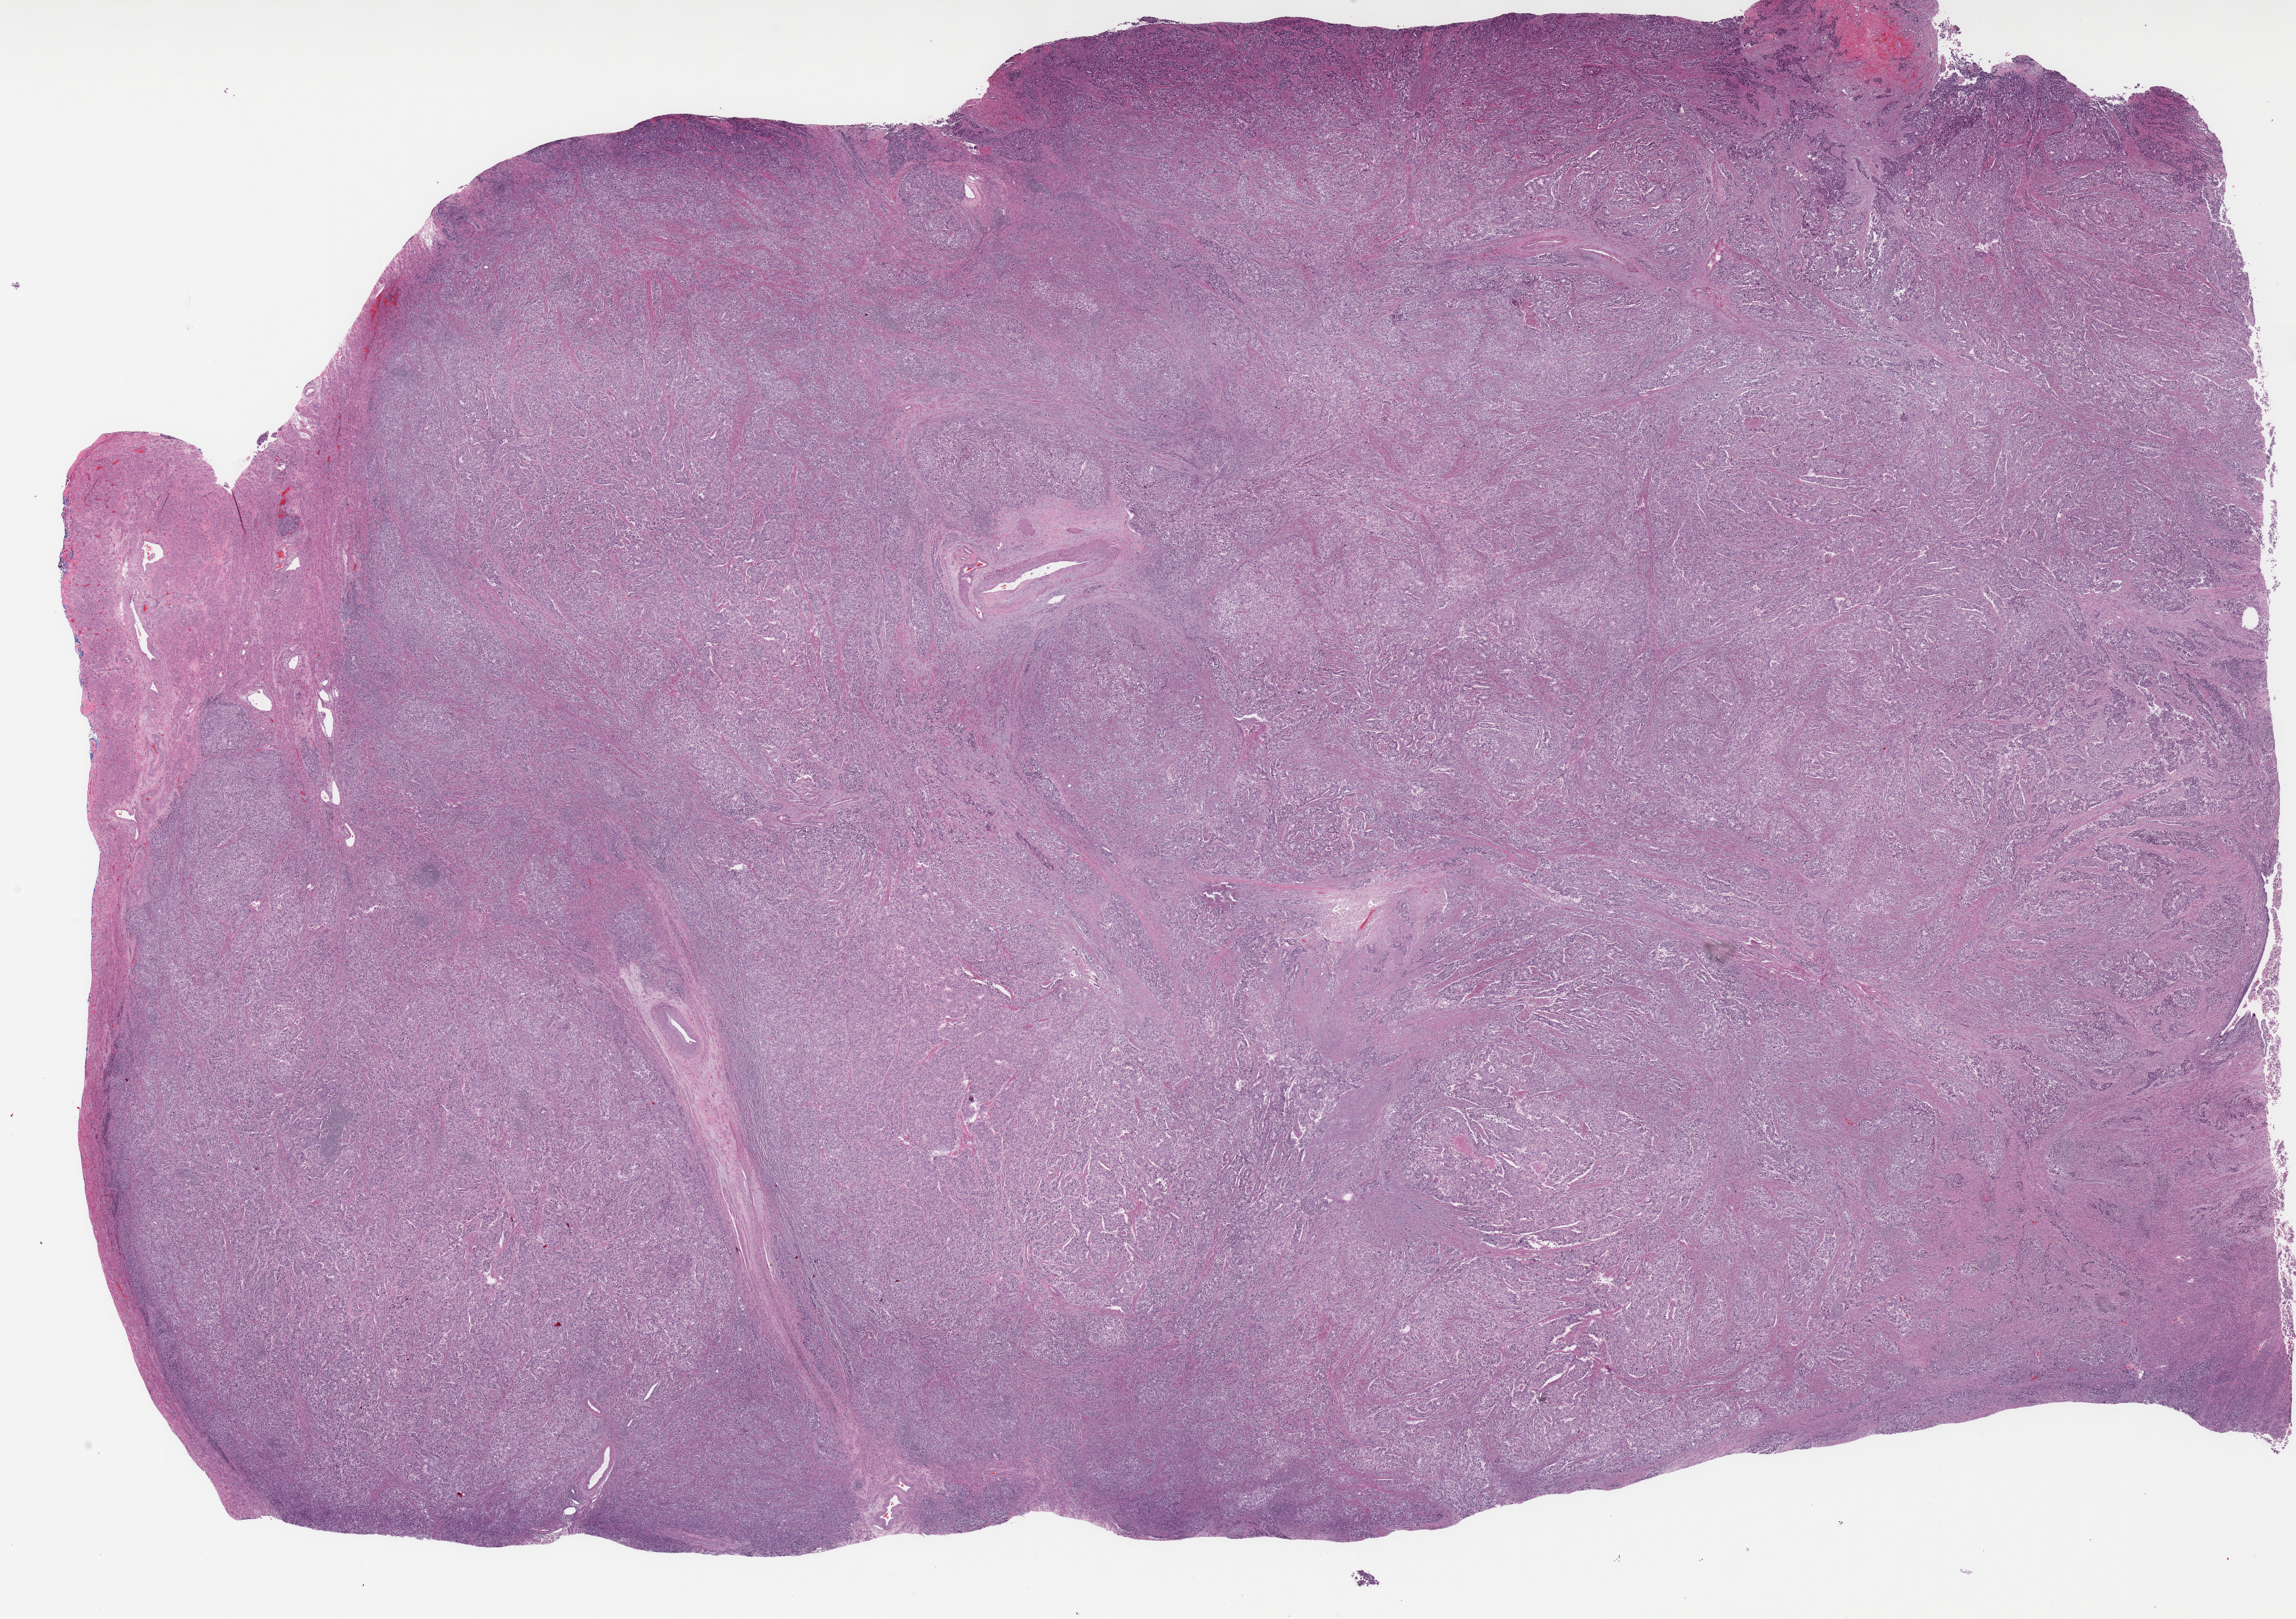
Whole-slide histology image, Hematoxylin and eosin (H&E) stained, low-resolution overview of the scanned area, about 27.8 x 19.6 mm (acquisition: 20x scan), formalin-fixed paraffin-embedded (FFPE) diagnostic section, sample: primary tumour, uterus. Patient: female, age at initial diagnosis 68 years. Histologic grade: G3 (poorly differentiated).
Pathologic diagnosis: Adenocarcinoma with mixed subtypes (endometrium). FIGO stage: IIIC1.